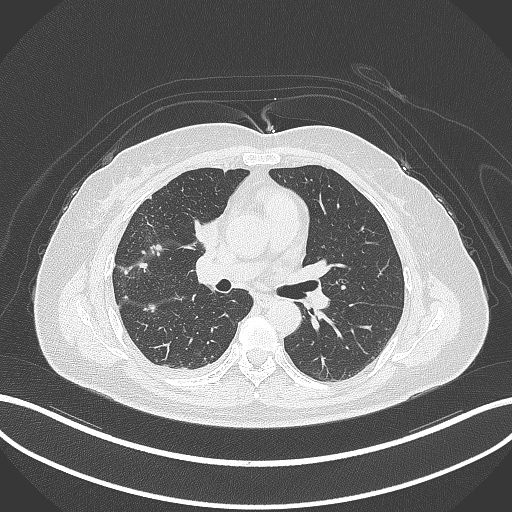
Chest CT, one axial slice; slice 153 of 305 in the series (ordered by position); lung window (W 1500 / L -600 HU); 512 × 512 image matrix, field of view 400 × 400 mm. Female patient, age 52 years. Case-level facts recorded for this patient, not image findings: clinical TNM (as recorded): T3 N1 M1.
Structures marked on this image (bounding box drawn by a radiologist):
- lung tumour (recorded histology: adenocarcinoma): box from (x=187, y=212) to (x=221, y=258) px